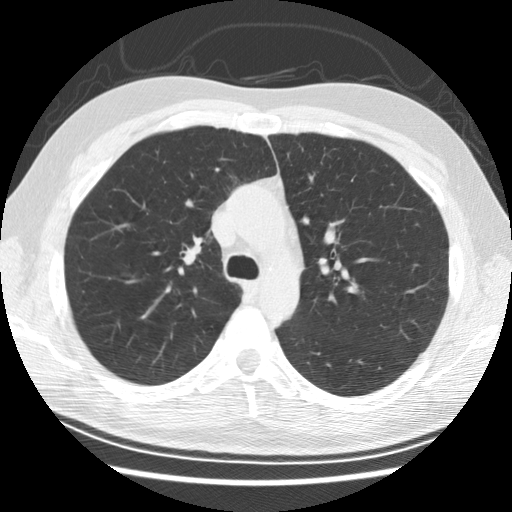
Axial slice from a low-dose chest CT screening exam, first (baseline) screen, lung window (W 1500 / L -600 HU), 2.5 mm slice thickness, 120 kVp, slice 91 of 278 in the series, 512 × 512 image matrix, field of view 340 × 340 mm. Male, age 57 years at enrolment. Former smoker at enrolment.
Lesion marked by an expert reader, box from (x=164, y=220) to (x=223, y=276) px. The screening reader recorded 6 non-calcified nodules or masses ≥4 mm on this exam (right middle lobe, right middle lobe, right lower lobe, right middle lobe, right middle lobe, right lower lobe); which of them this box marks is not recorded. Official screen result: negative screen, minor abnormalities not suspicious for lung cancer. Lung cancer was diagnosed 766 days after this screen: adenocarcinoma, NOS, right upper lobe, poorly differentiated (G3), stage IB (AJCC 6th edition), 25 mm at pathology.